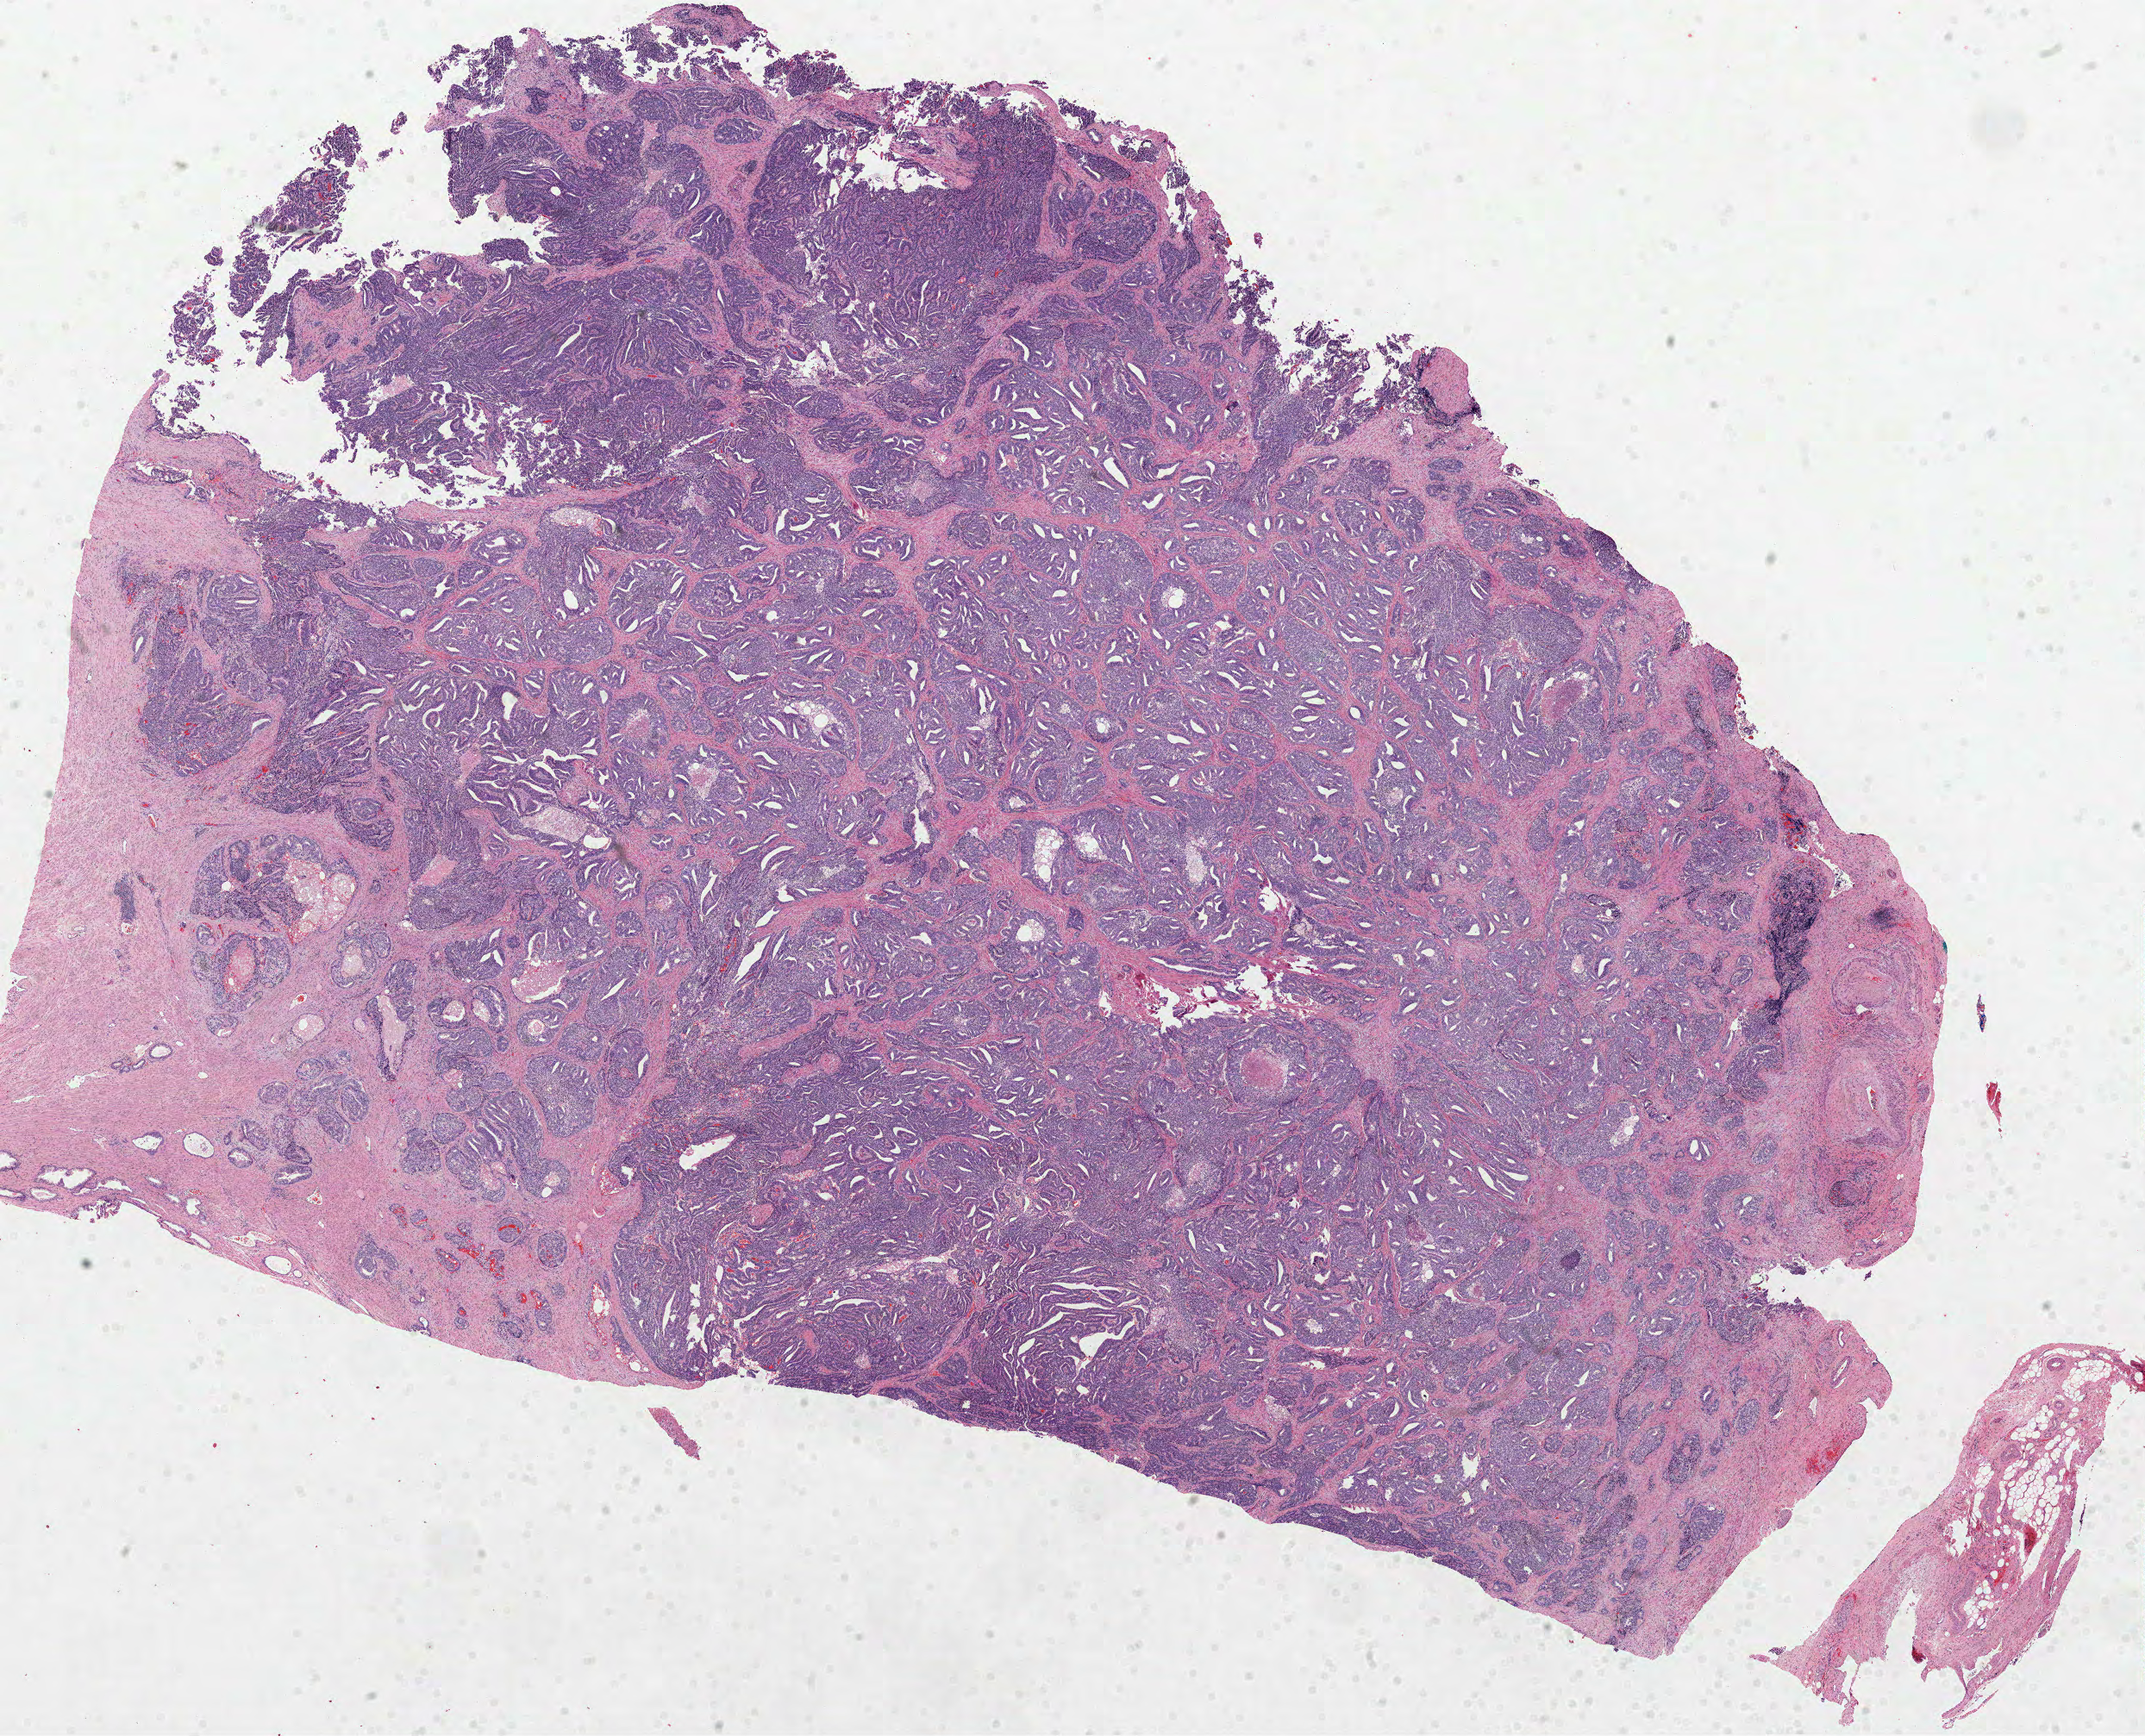
H&E whole-slide image — a low-resolution overview of the entire scanned area, about 20.1 x 16.2 mm, formalin-fixed paraffin-embedded (FFPE) diagnostic section, prostate, primary tumour sample. Male, age 67 years at initial diagnosis. Gleason score: 9 (4+5).
Pathologic diagnosis: Acinar cell carcinoma (prostate gland). Lymph nodes positive (case pathology): 0 of 8 examined.